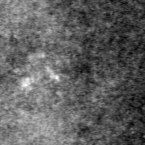
Region of interest cut from a scanned film mammogram (one marked finding); right breast; CC view.
Finding: calcifications, morphology pleomorphic, distribution clustered; BI-RADS assessment category 3; subtlety rating 1 on a 1 (subtle) to 5 (obvious) scale; pathology result (as recorded, not read from the image): benign.